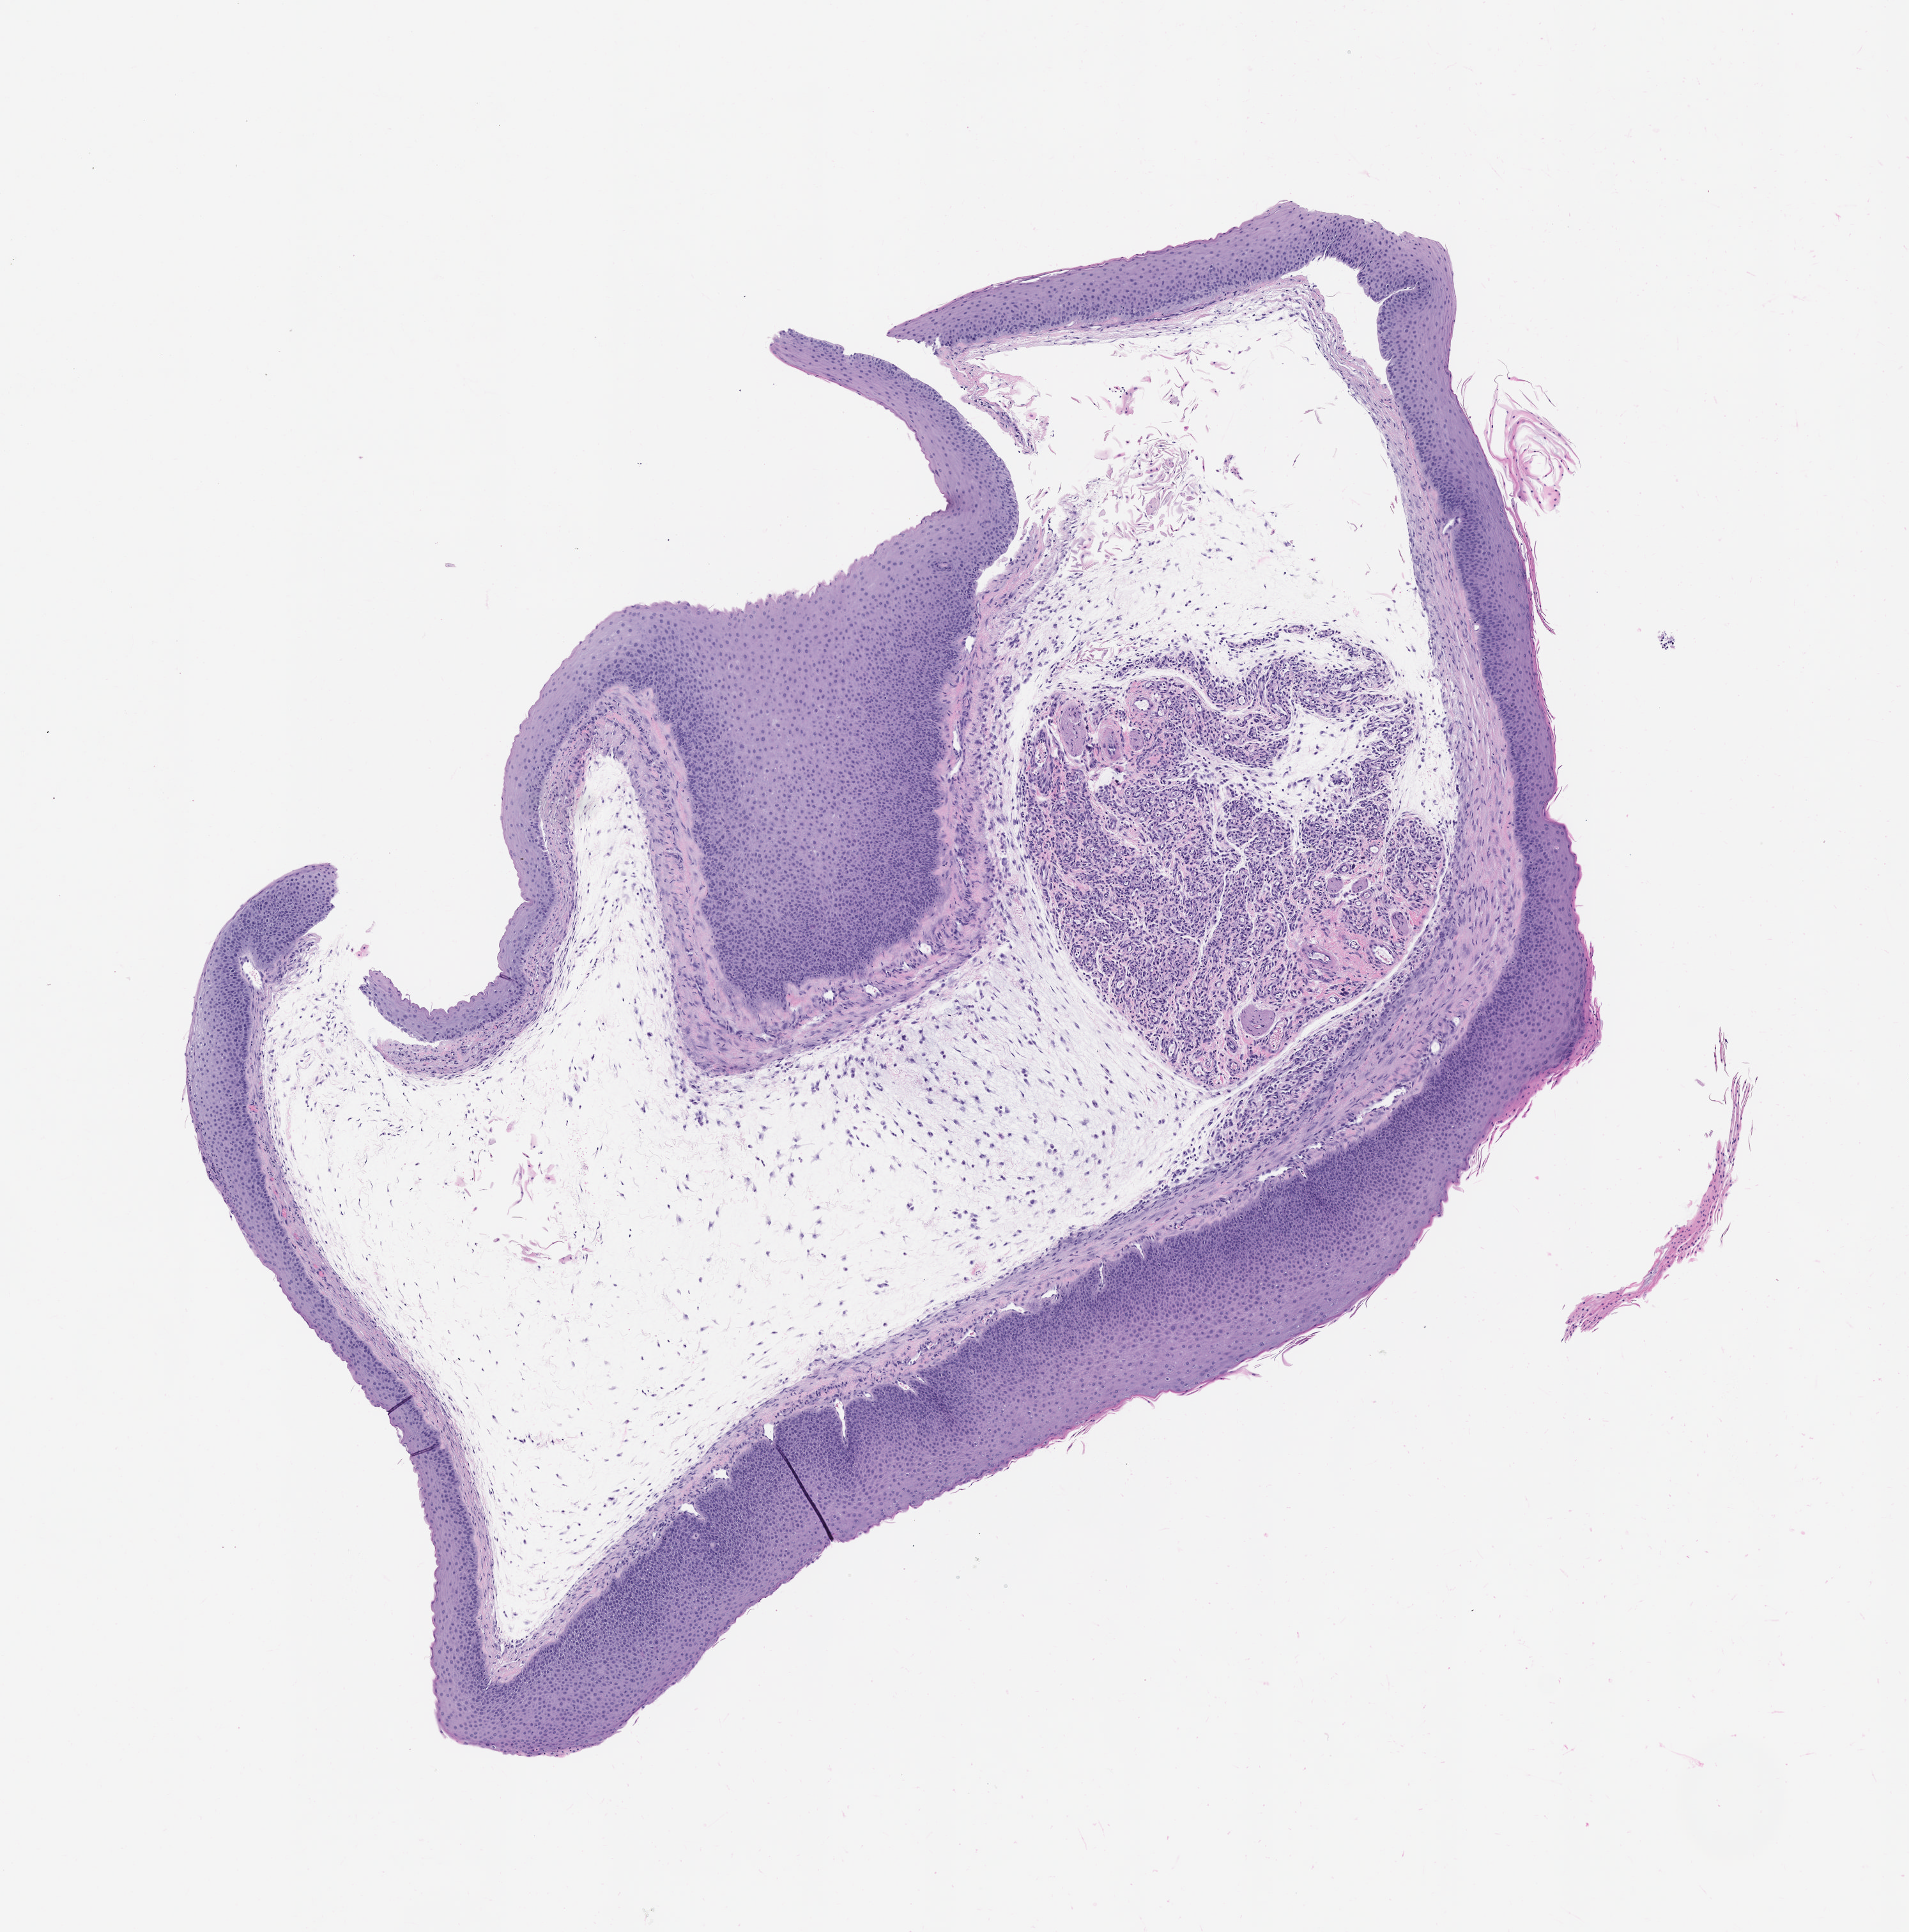
Whole-slide image, haematoxylin and eosin: patient-derived xenograft (human tumor grown in a mouse), passage 1, a low-resolution overview of the entire scanned area, about 6.0 x 6.1 mm. Formalin-fixed, paraffin-embedded (FFPE) tissue. Tumor site category: bladder.
Originating patient diagnosis: Transitional Cell Carcinoma.